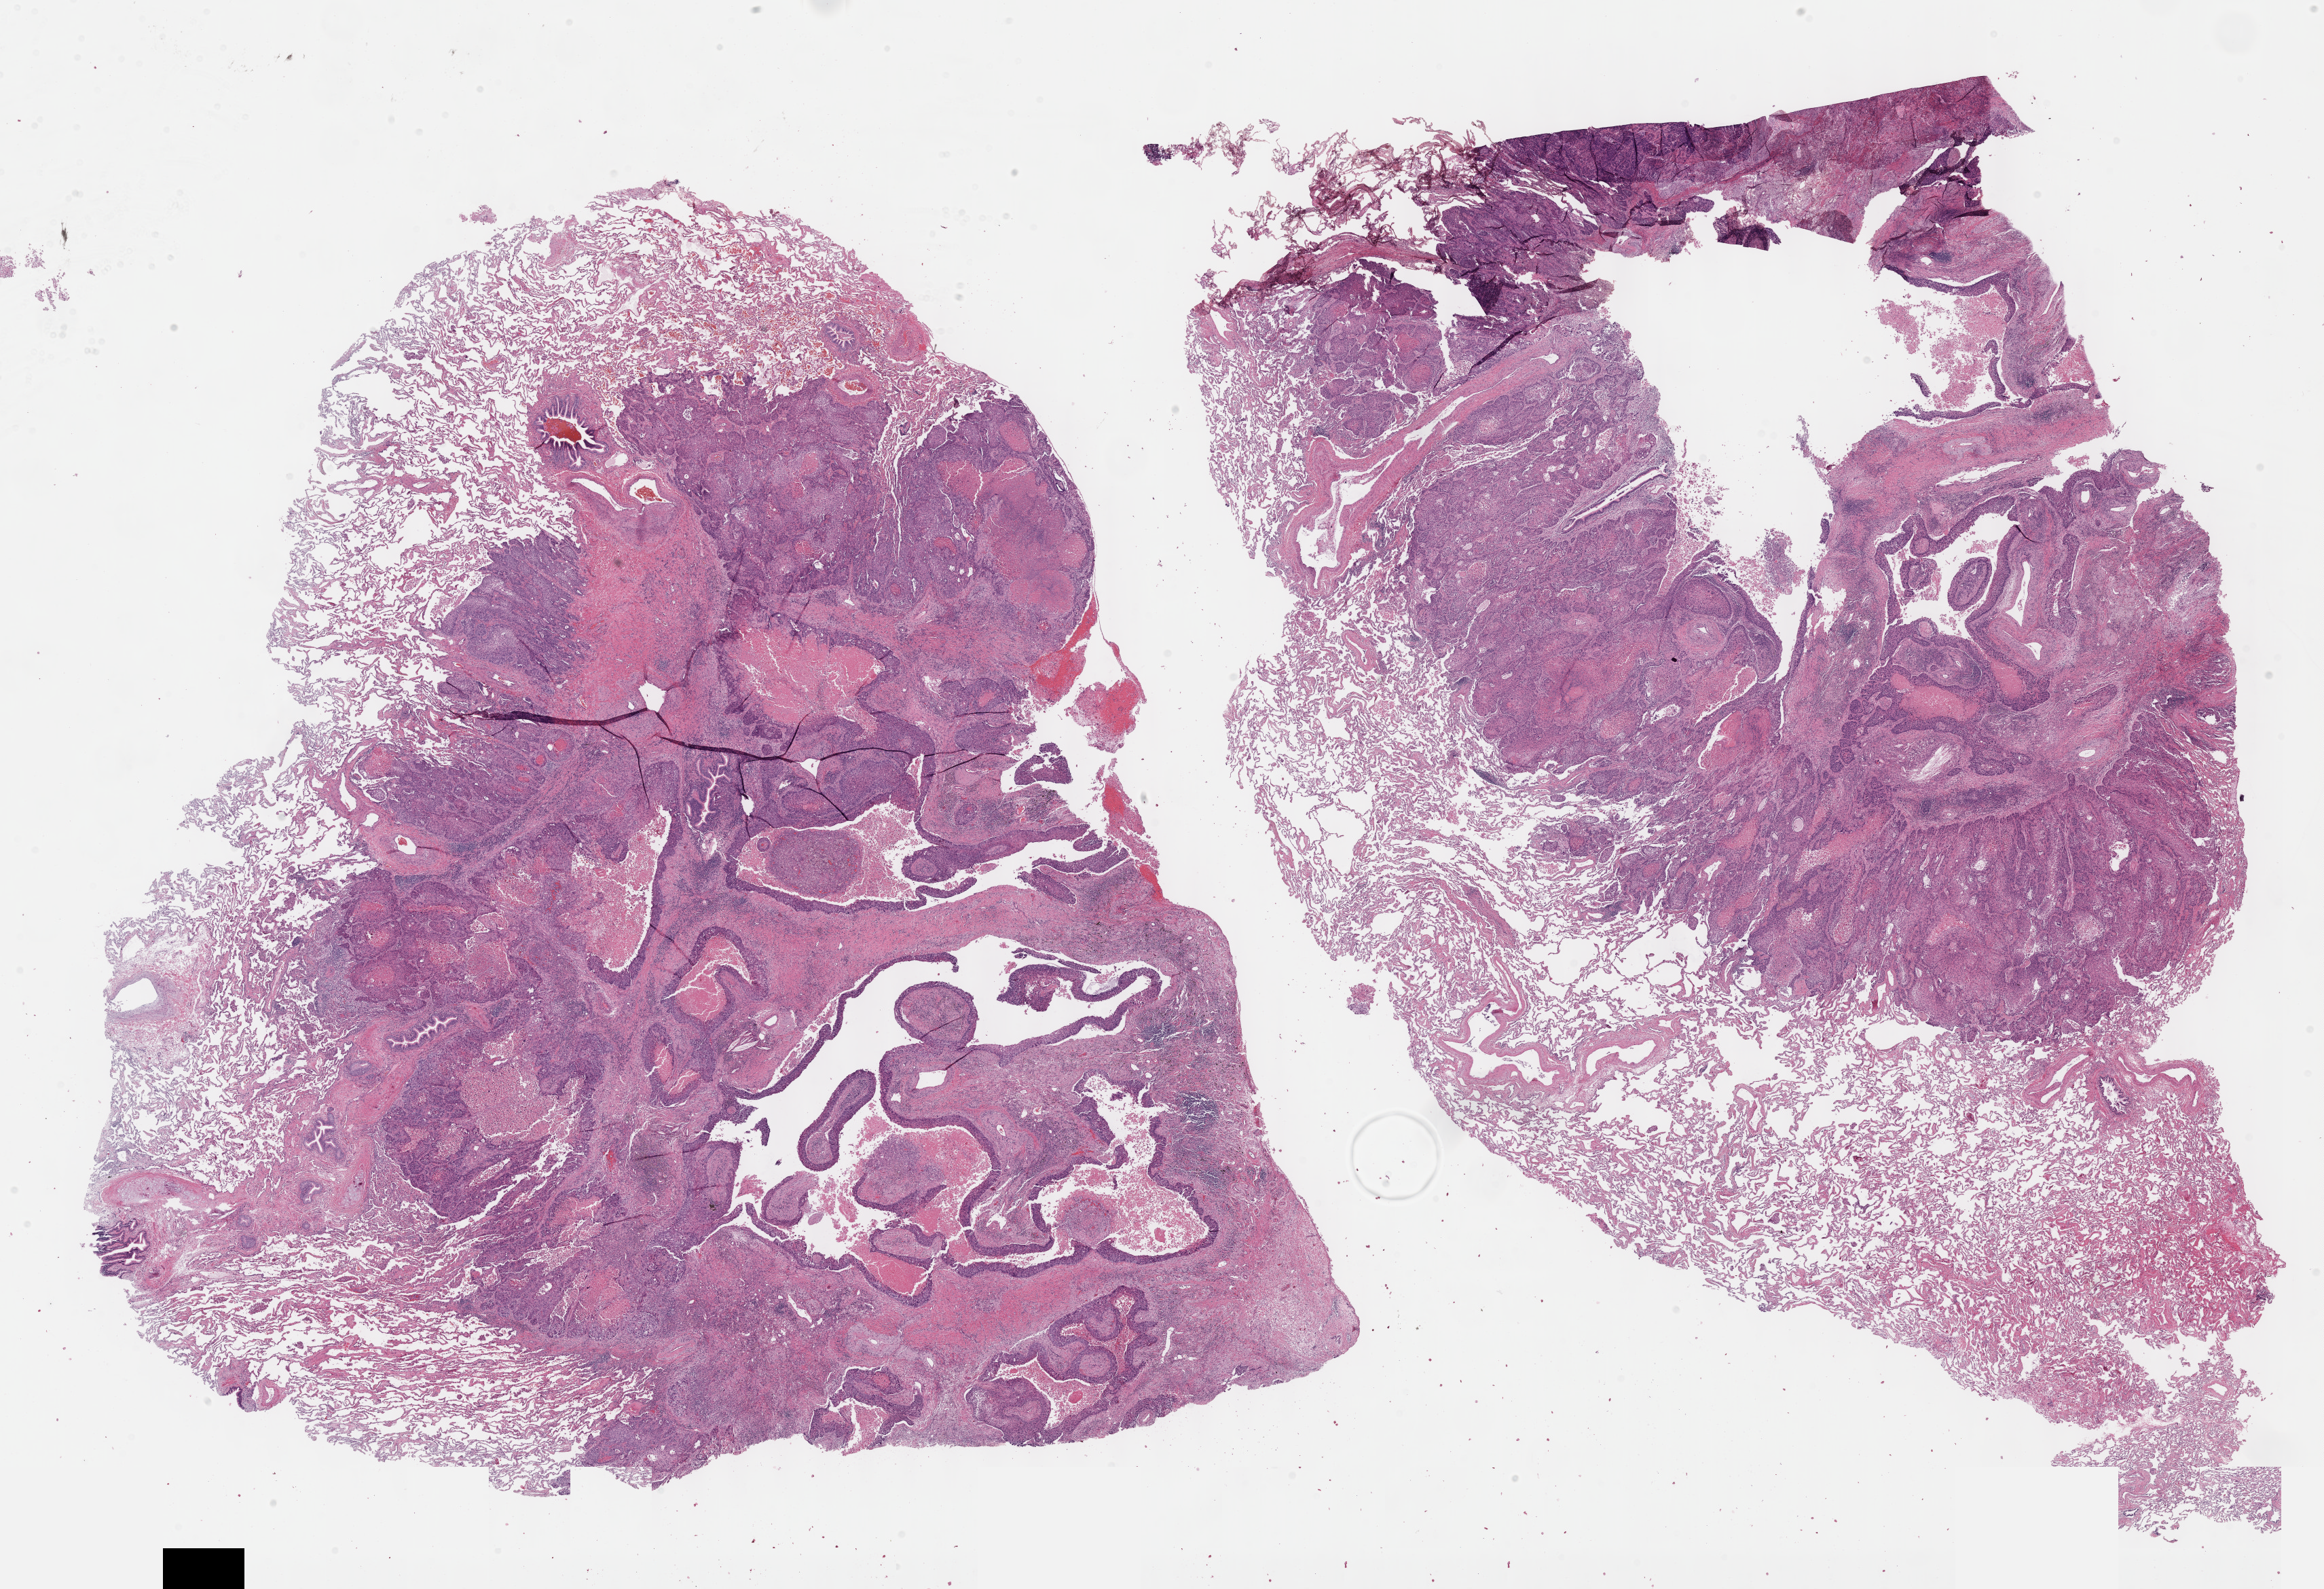
Digitized H&E tissue section (whole slide) — shown as a low-resolution overview of the whole scanned area (about 27.7 x 18.9 mm, slide scanned at 40x). Formalin-fixed paraffin-embedded (FFPE) diagnostic section. Primary tumour sample from the lung. Female, age 78 years at initial diagnosis.
AJCC pathologic stage: IB. Diagnosis: Squamous cell carcinoma, large cell, nonkeratinizing, NOS (upper lobe, lung). Laterality: right.